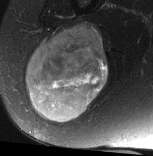
MRI of an extremity soft-tissue mass, one axial slice. Position 33 of 77 along the scan axis. T2-weighted fat-saturated. MR volume resampled by the dataset authors to the PET/CT grid (not the native acquisition matrix). 153 × 156 image matrix. Female patient. From the clinical record (not read from this slice): histological type: synovial sarcoma; grade: intermediate; site of the primary tumour: right buttock.
Annotated regions visible in this slice (expert contour drawn on MRI and transferred to this co-registered scan by the dataset authors):
- gross tumour volume including surrounding oedema: bounding box <26,24,109,123> (left, top, right, bottom; pixels)
- gross tumour volume (mass): <26,24,109,123>